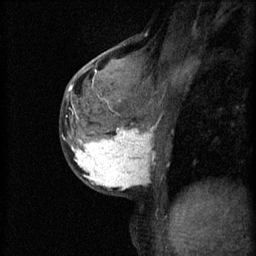
Breast MRI (dynamic contrast-enhanced), one sagittal slice; slice 31 of 60 in the series (ordered by position); 3 images stored at this slice position (order not interpretable as contrast timing); 1.5 T; TE 4.2 ms, TR 11 ms; 2 mm slice thickness; 256 × 256 image matrix, field of view 180 × 180 mm. Female patient, age 37 years.
Outlined on this slice (semi-automatic segmentation, software-assisted and operator-edited):
- analysis volume of interest (the breast-tissue region the enhancement analysis was run in; not a lesion): bounding box (x1, y1, x2, y2) in pixels: (68, 118, 163, 195)
- tumour enhancement mask (voxels above the 70 % enhancement threshold inside the analysis volume of interest): (71, 118, 154, 191)